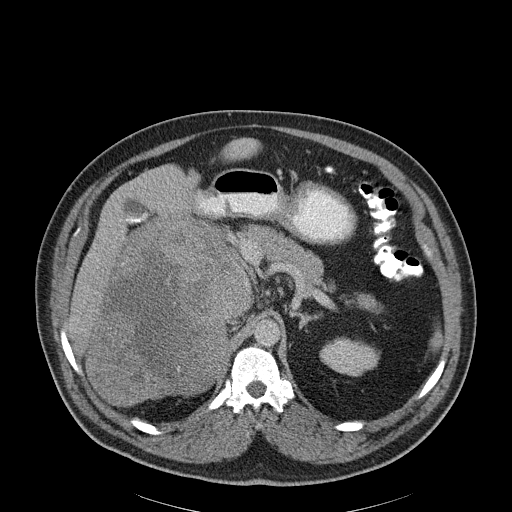
Contrast-enhanced abdominal CT, one axial slice; position 133 of 186 along the scan axis; reconstruction kernel B30f; 120 kVp; soft-tissue window (W 400 / L 40 HU); 3 mm slice thickness; 512 × 512 image matrix, field of view 464 × 464 mm. Patient: male, 56 years. From the clinical record (not read from this slice): diagnosis: adrenocortical carcinoma; tumour side: right adrenal; tumour size at pathology: 18 cm; Ki-67 index: 2 %; stage (as recorded): 3.
Outlined on this slice (semi-automatic segmentation, software-assisted and operator-edited):
- mass: box from (x=89, y=222) to (x=247, y=405) px